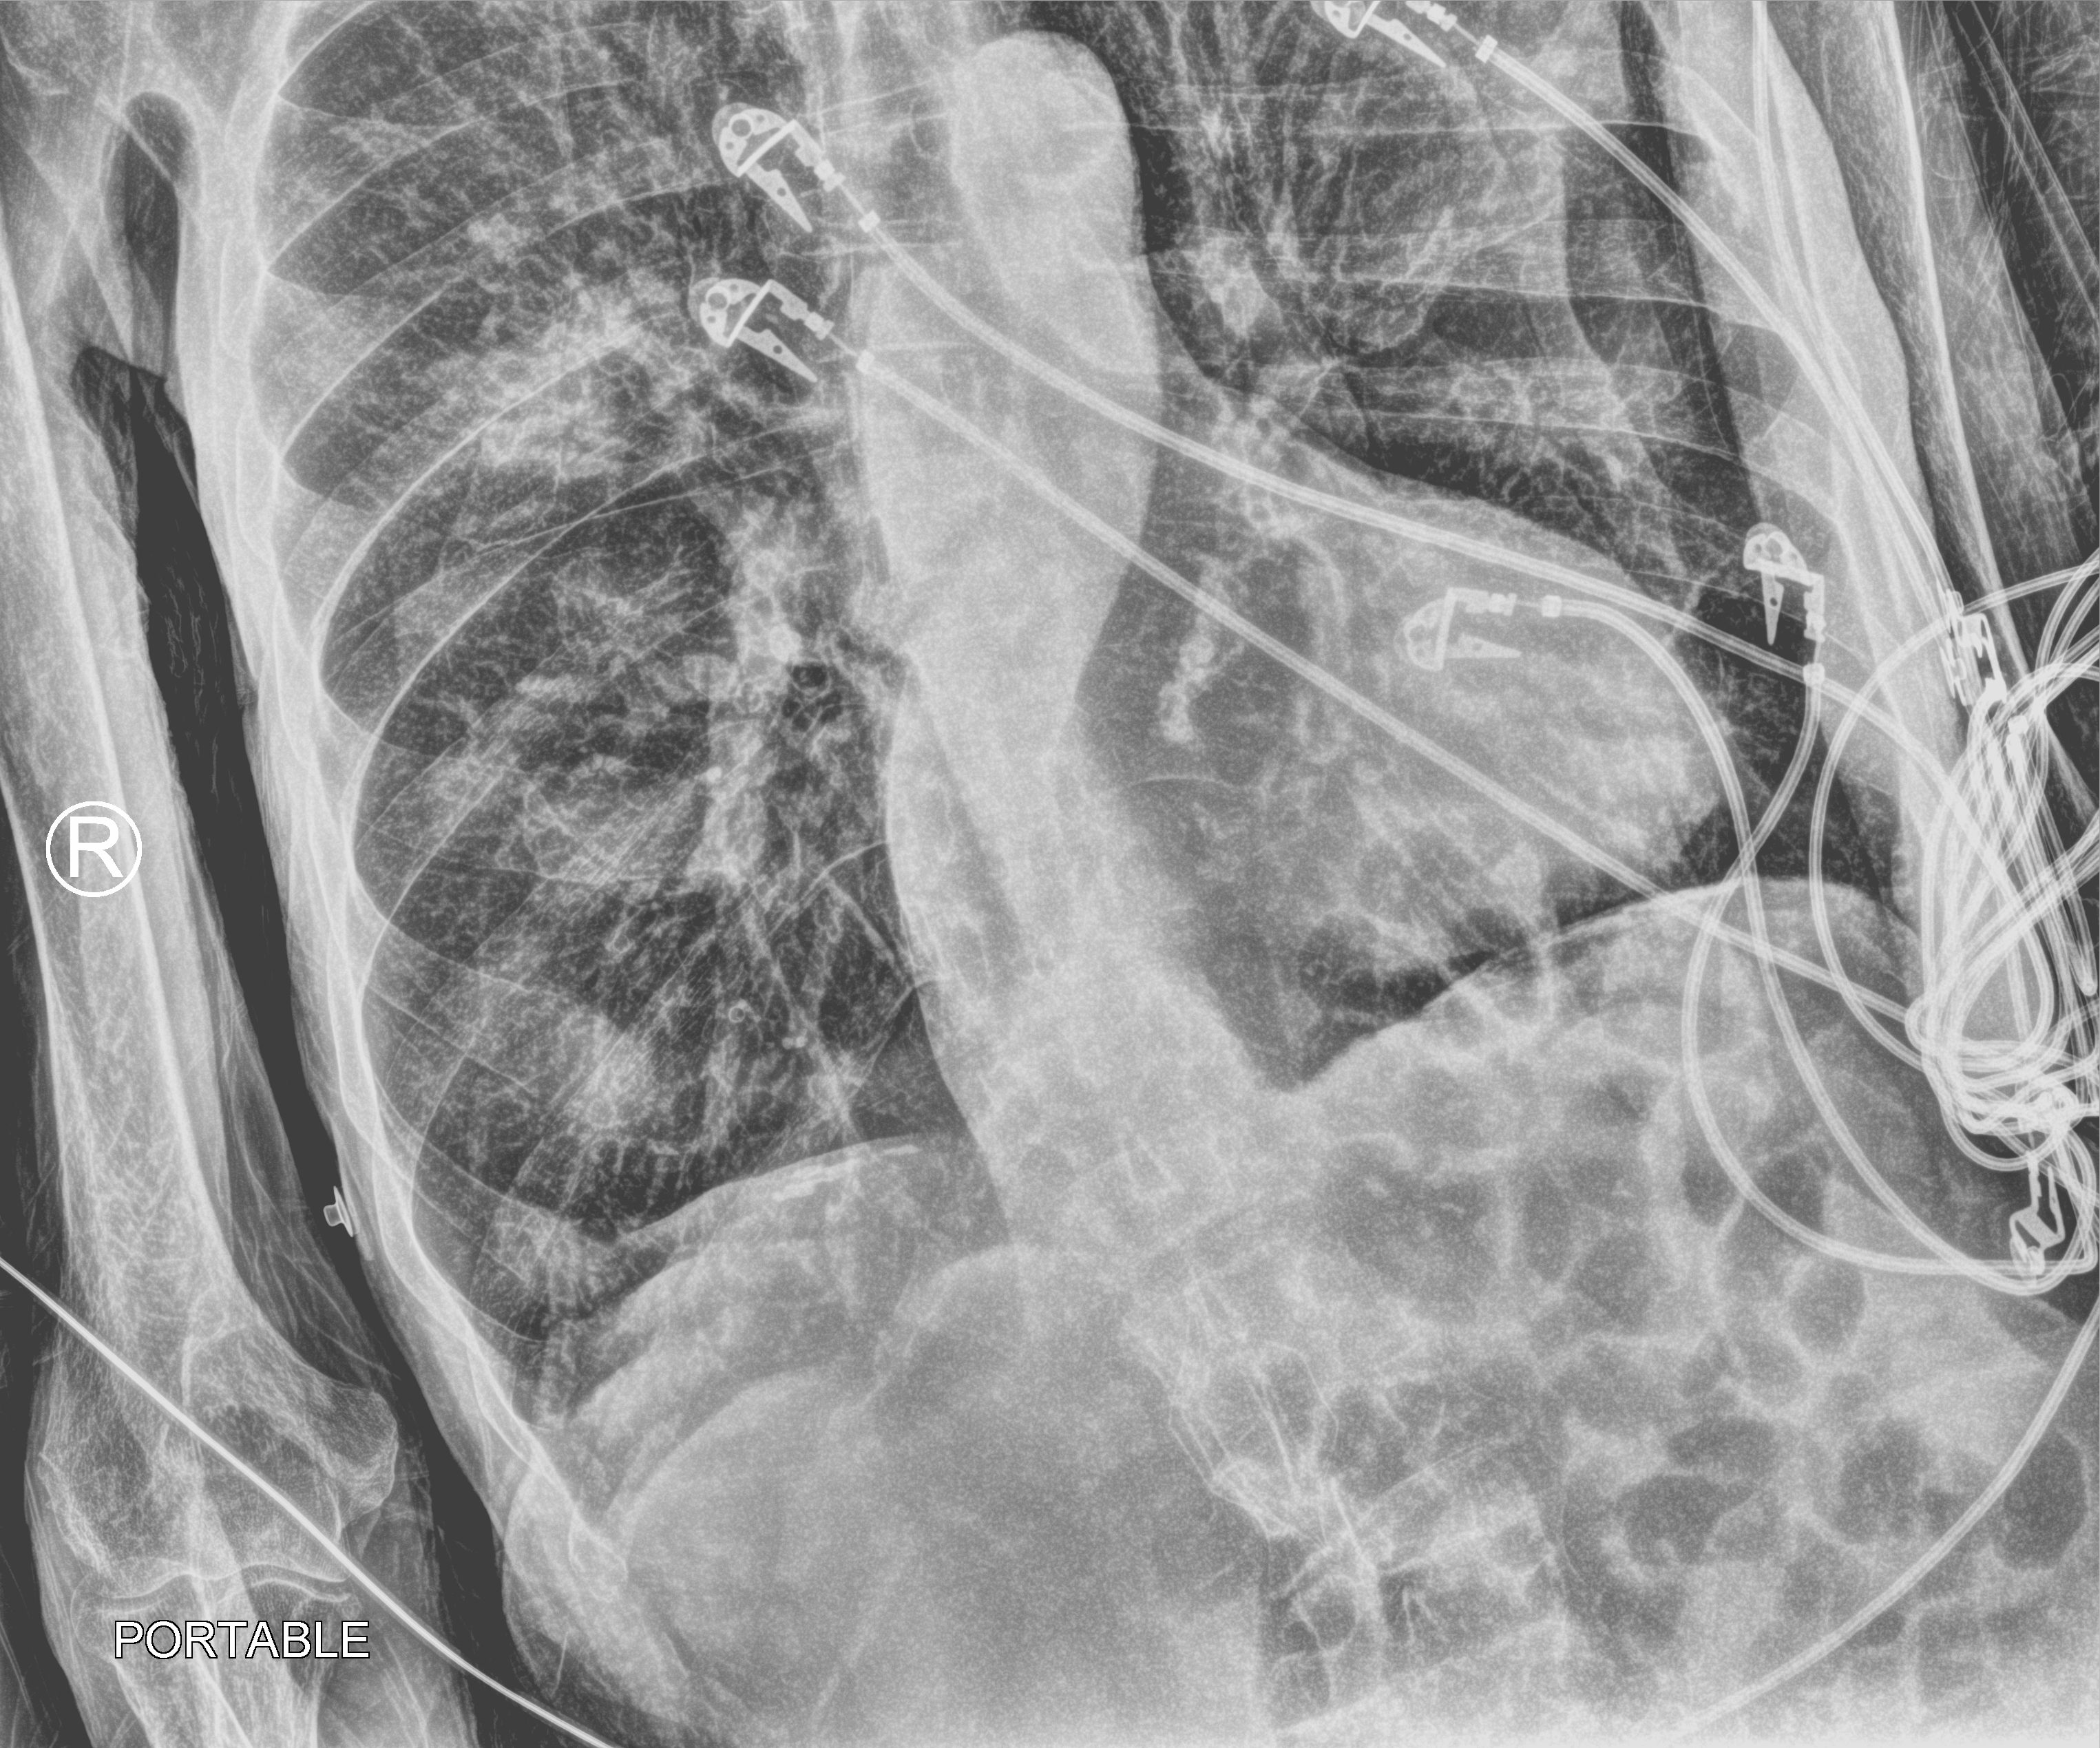
Bedside chest radiograph (computed radiography); anteroposterior (AP) projection. Male patient hospitalised with COVID-19, age 75–90 years.
From the hospital-stay record, not from the radiograph (when in the stay this image was taken is not recorded): smoking status (admission record): former; mechanically ventilated during this hospital stay: no.